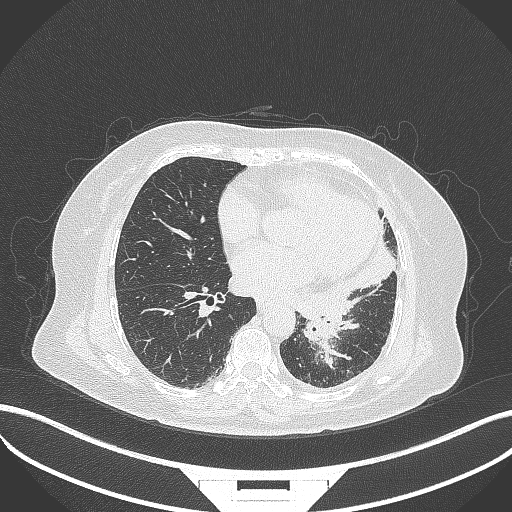
Chest CT, one axial slice. Slice 150 of 322 in the series (ordered by position). 120 kVp. Lung window (W 1500 / L -600 HU). 1 mm slice thickness. 512 × 512 image matrix. Patient: female, 69 years. Case-level facts recorded for this patient, not image findings: clinical TNM (as recorded): T2b N3 M1.
Structures marked on this image (bounding box drawn by a radiologist):
- lung tumour (recorded histology: adenocarcinoma): bounding box [x1, y1, x2, y2] px = [300, 309, 345, 346]